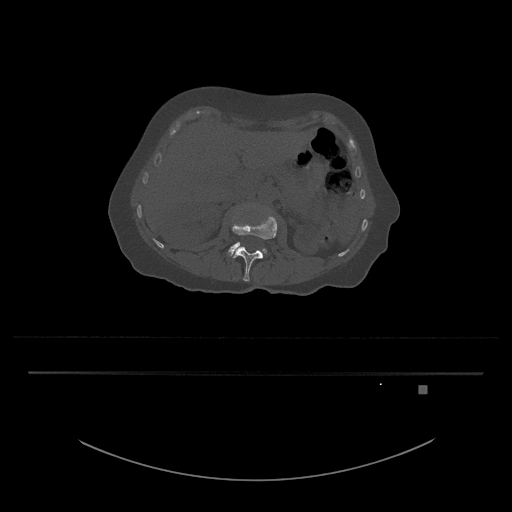
CT including the spine, one axial slice; slice 475 of 797 in the series (ordered by position); reconstruction kernel Br40s/3; 120 kVp; bone window (W 1800 / L 400 HU); 0.5 mm slice thickness; 512 × 512 image matrix. Patient: female, 57 years. From the clinical record (not read from this slice): primary cancer: cervical.
Outlined on this slice (semi-automatically segmented with operator editing):
- L3 vertebra: box from (x=228, y=242) to (x=267, y=257) px